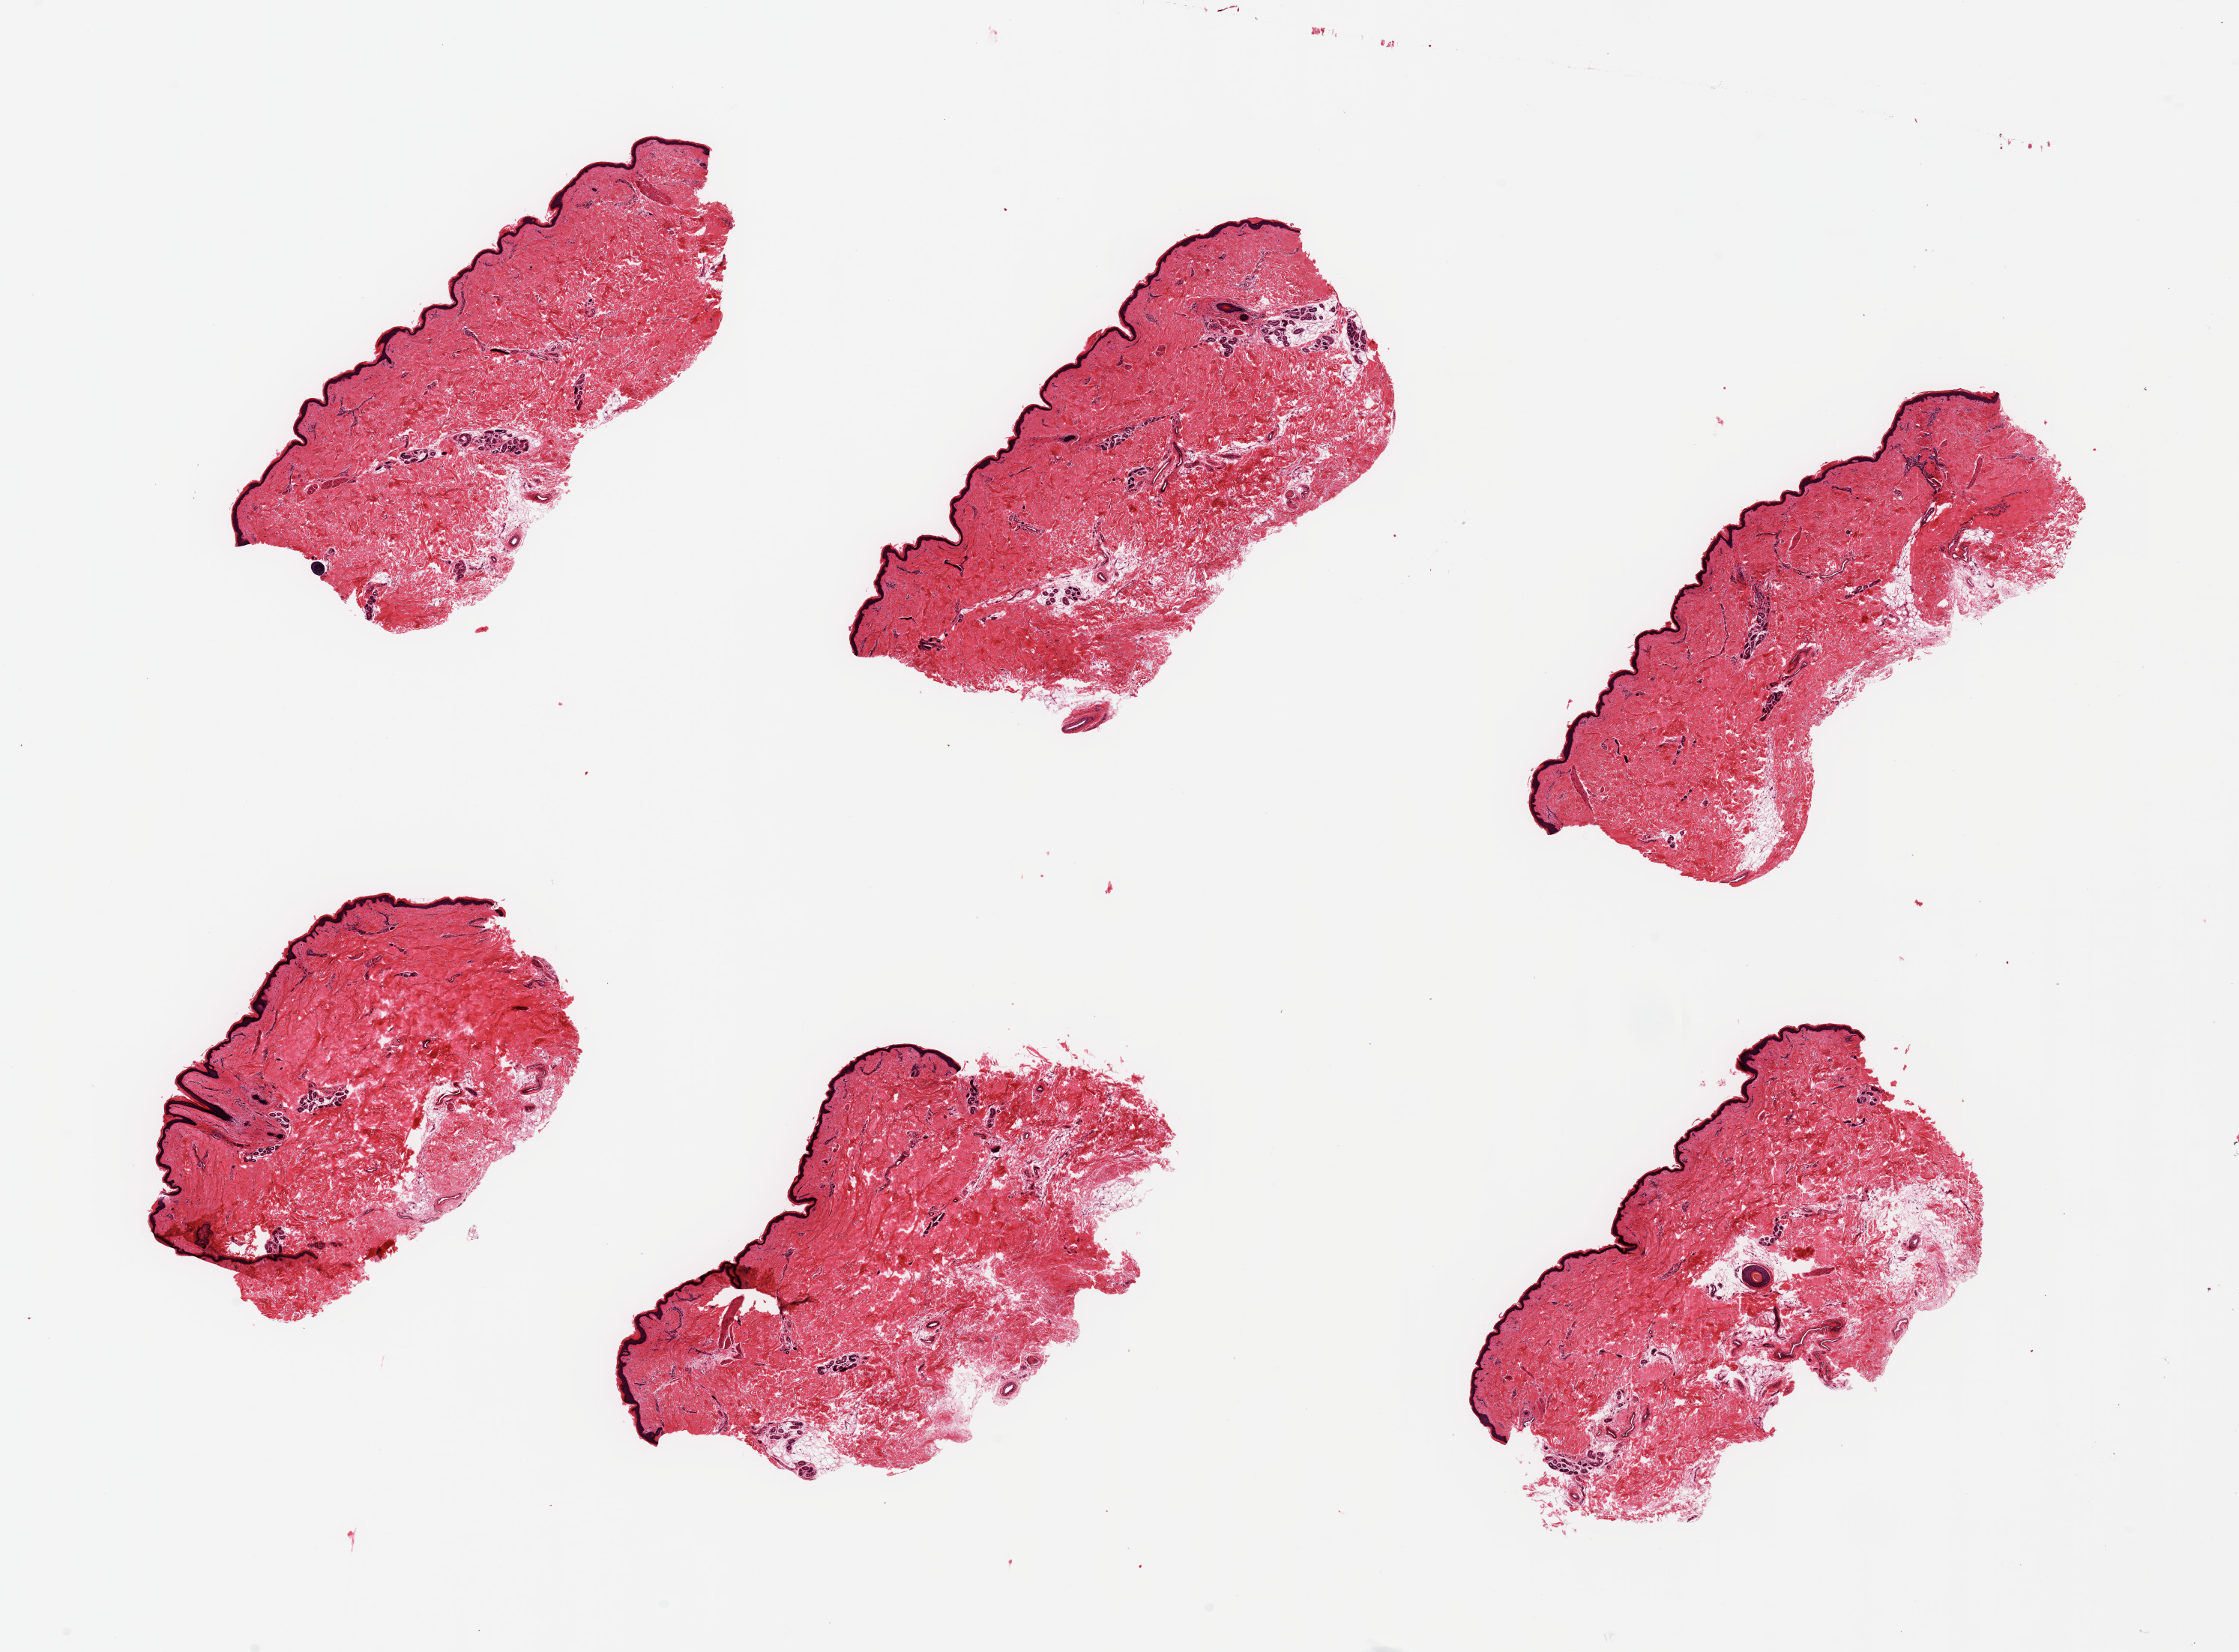
Hematoxylin and eosin (H&E) whole-slide image — low-resolution overview of the scanned area, about 23.6 x 17.4 mm, PAXgene-fixed, paraffin-embedded tissue, section of skin of lower leg (target tissue), tissue donor sample. Donor: male.
Review note (as recorded): 6 pieces, no significant dermal fat; squamous epithelium is ~45-50 microns.